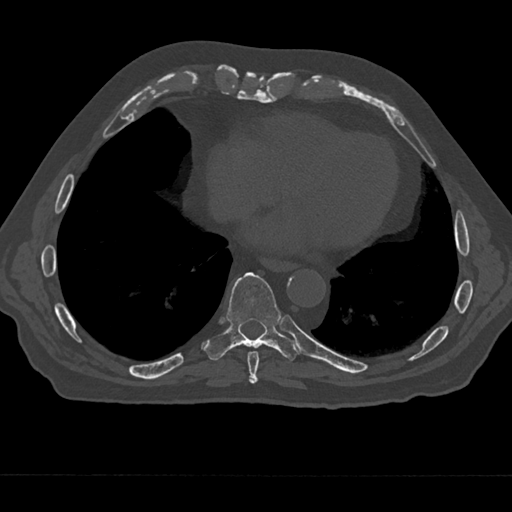
CT including the spine, one axial slice. Position 276 of 797 along the scan axis. Reconstruction kernel Br40s/3. 120 kVp. Bone window (W 1800 / L 400 HU). 0.5 mm slice thickness. 512 × 512 image matrix. Male patient, age 75 years. From the clinical record (not read from this slice): primary cancer: renal.
Annotated regions visible in this slice (semi-automatic segmentation, software-assisted and operator-edited):
- T8 vertebra: box from (x=247, y=351) to (x=259, y=383) px
- T9 vertebra: (x=204, y=272)–(x=299, y=360)